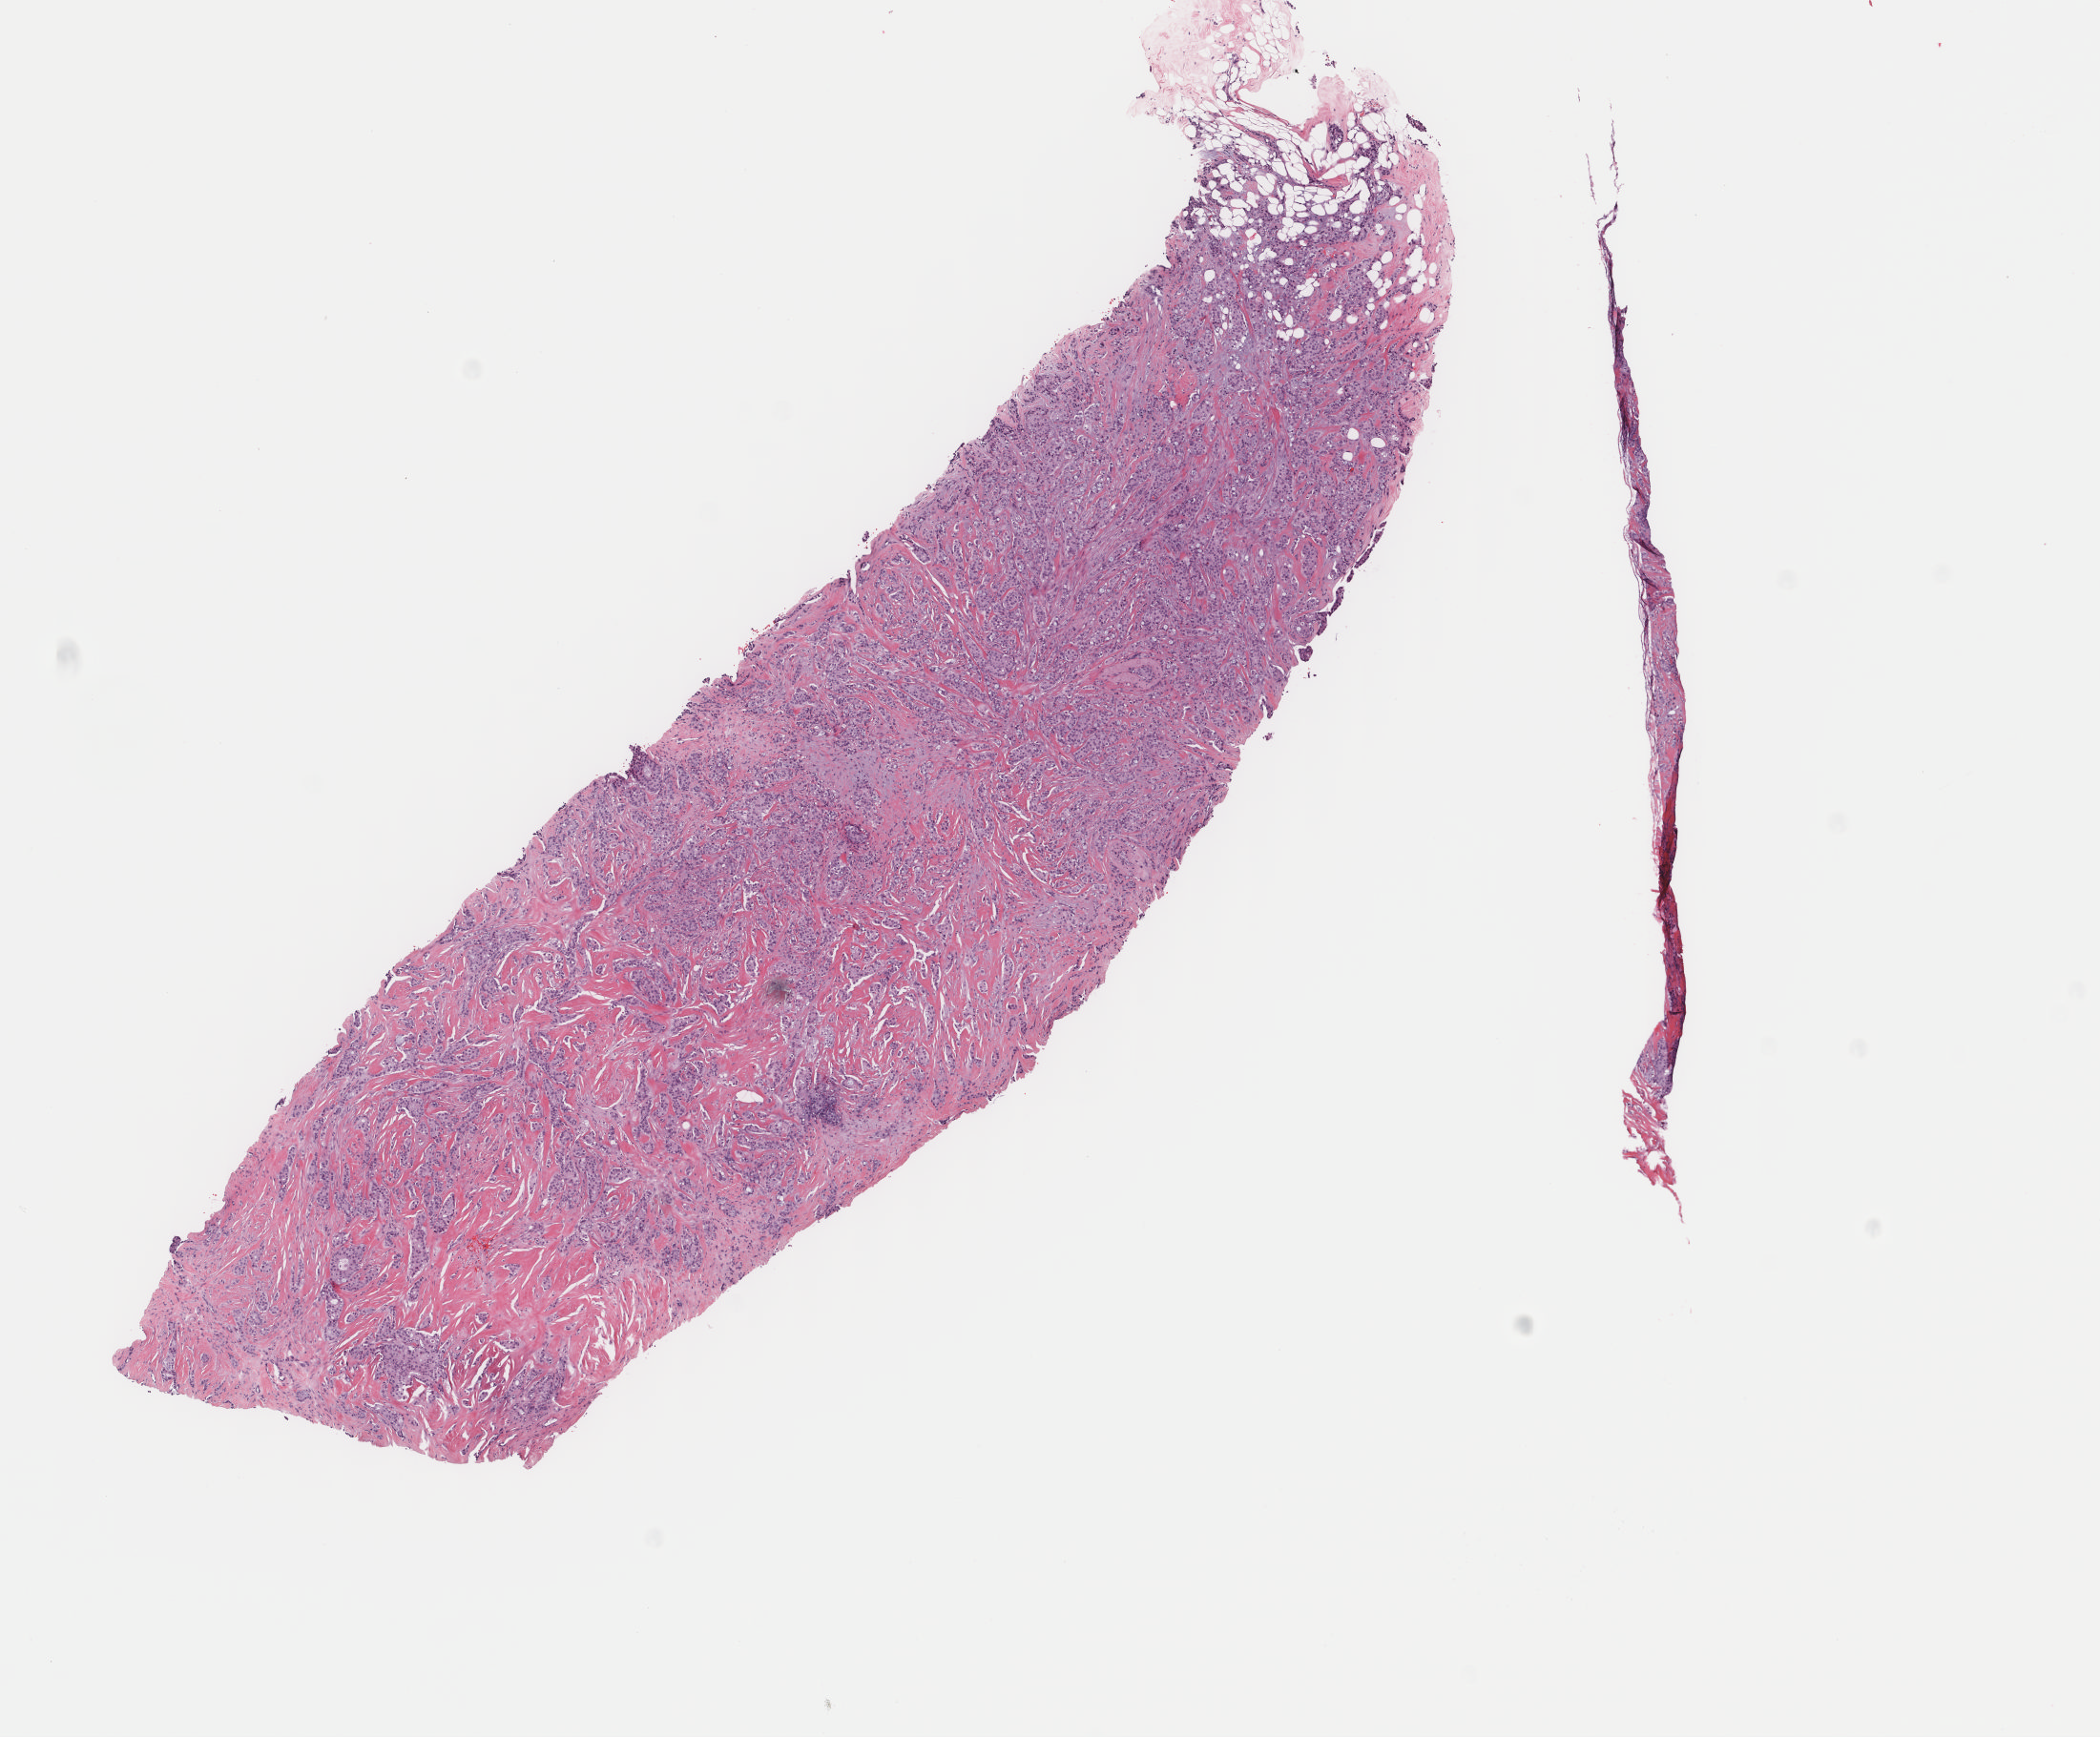
Whole-slide histology image, H&E, whole scanned area (about 8.7 x 7.2 mm, from a 40x scan) shown as a low-resolution overview; frozen section; sample: primary tumour, breast. Female patient; age at initial diagnosis 56 years.
Histologic diagnosis: Infiltrating duct carcinoma, NOS.